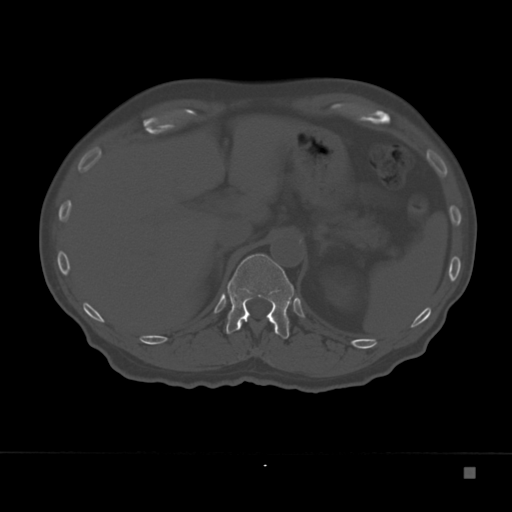
CT including the spine, one axial slice. Position 137 of 332 along the scan axis. Reconstruction kernel Br40s. Bone window (W 1800 / L 400 HU). 512 × 512 image matrix, field of view 389 × 389 mm. Patient: male, 72 years. From the clinical record (not read from this slice): primary cancer: skeletal.
Outlined on this slice (semi-automatically segmented with operator editing):
- T12 vertebra: box from (x=226, y=254) to (x=294, y=339) px